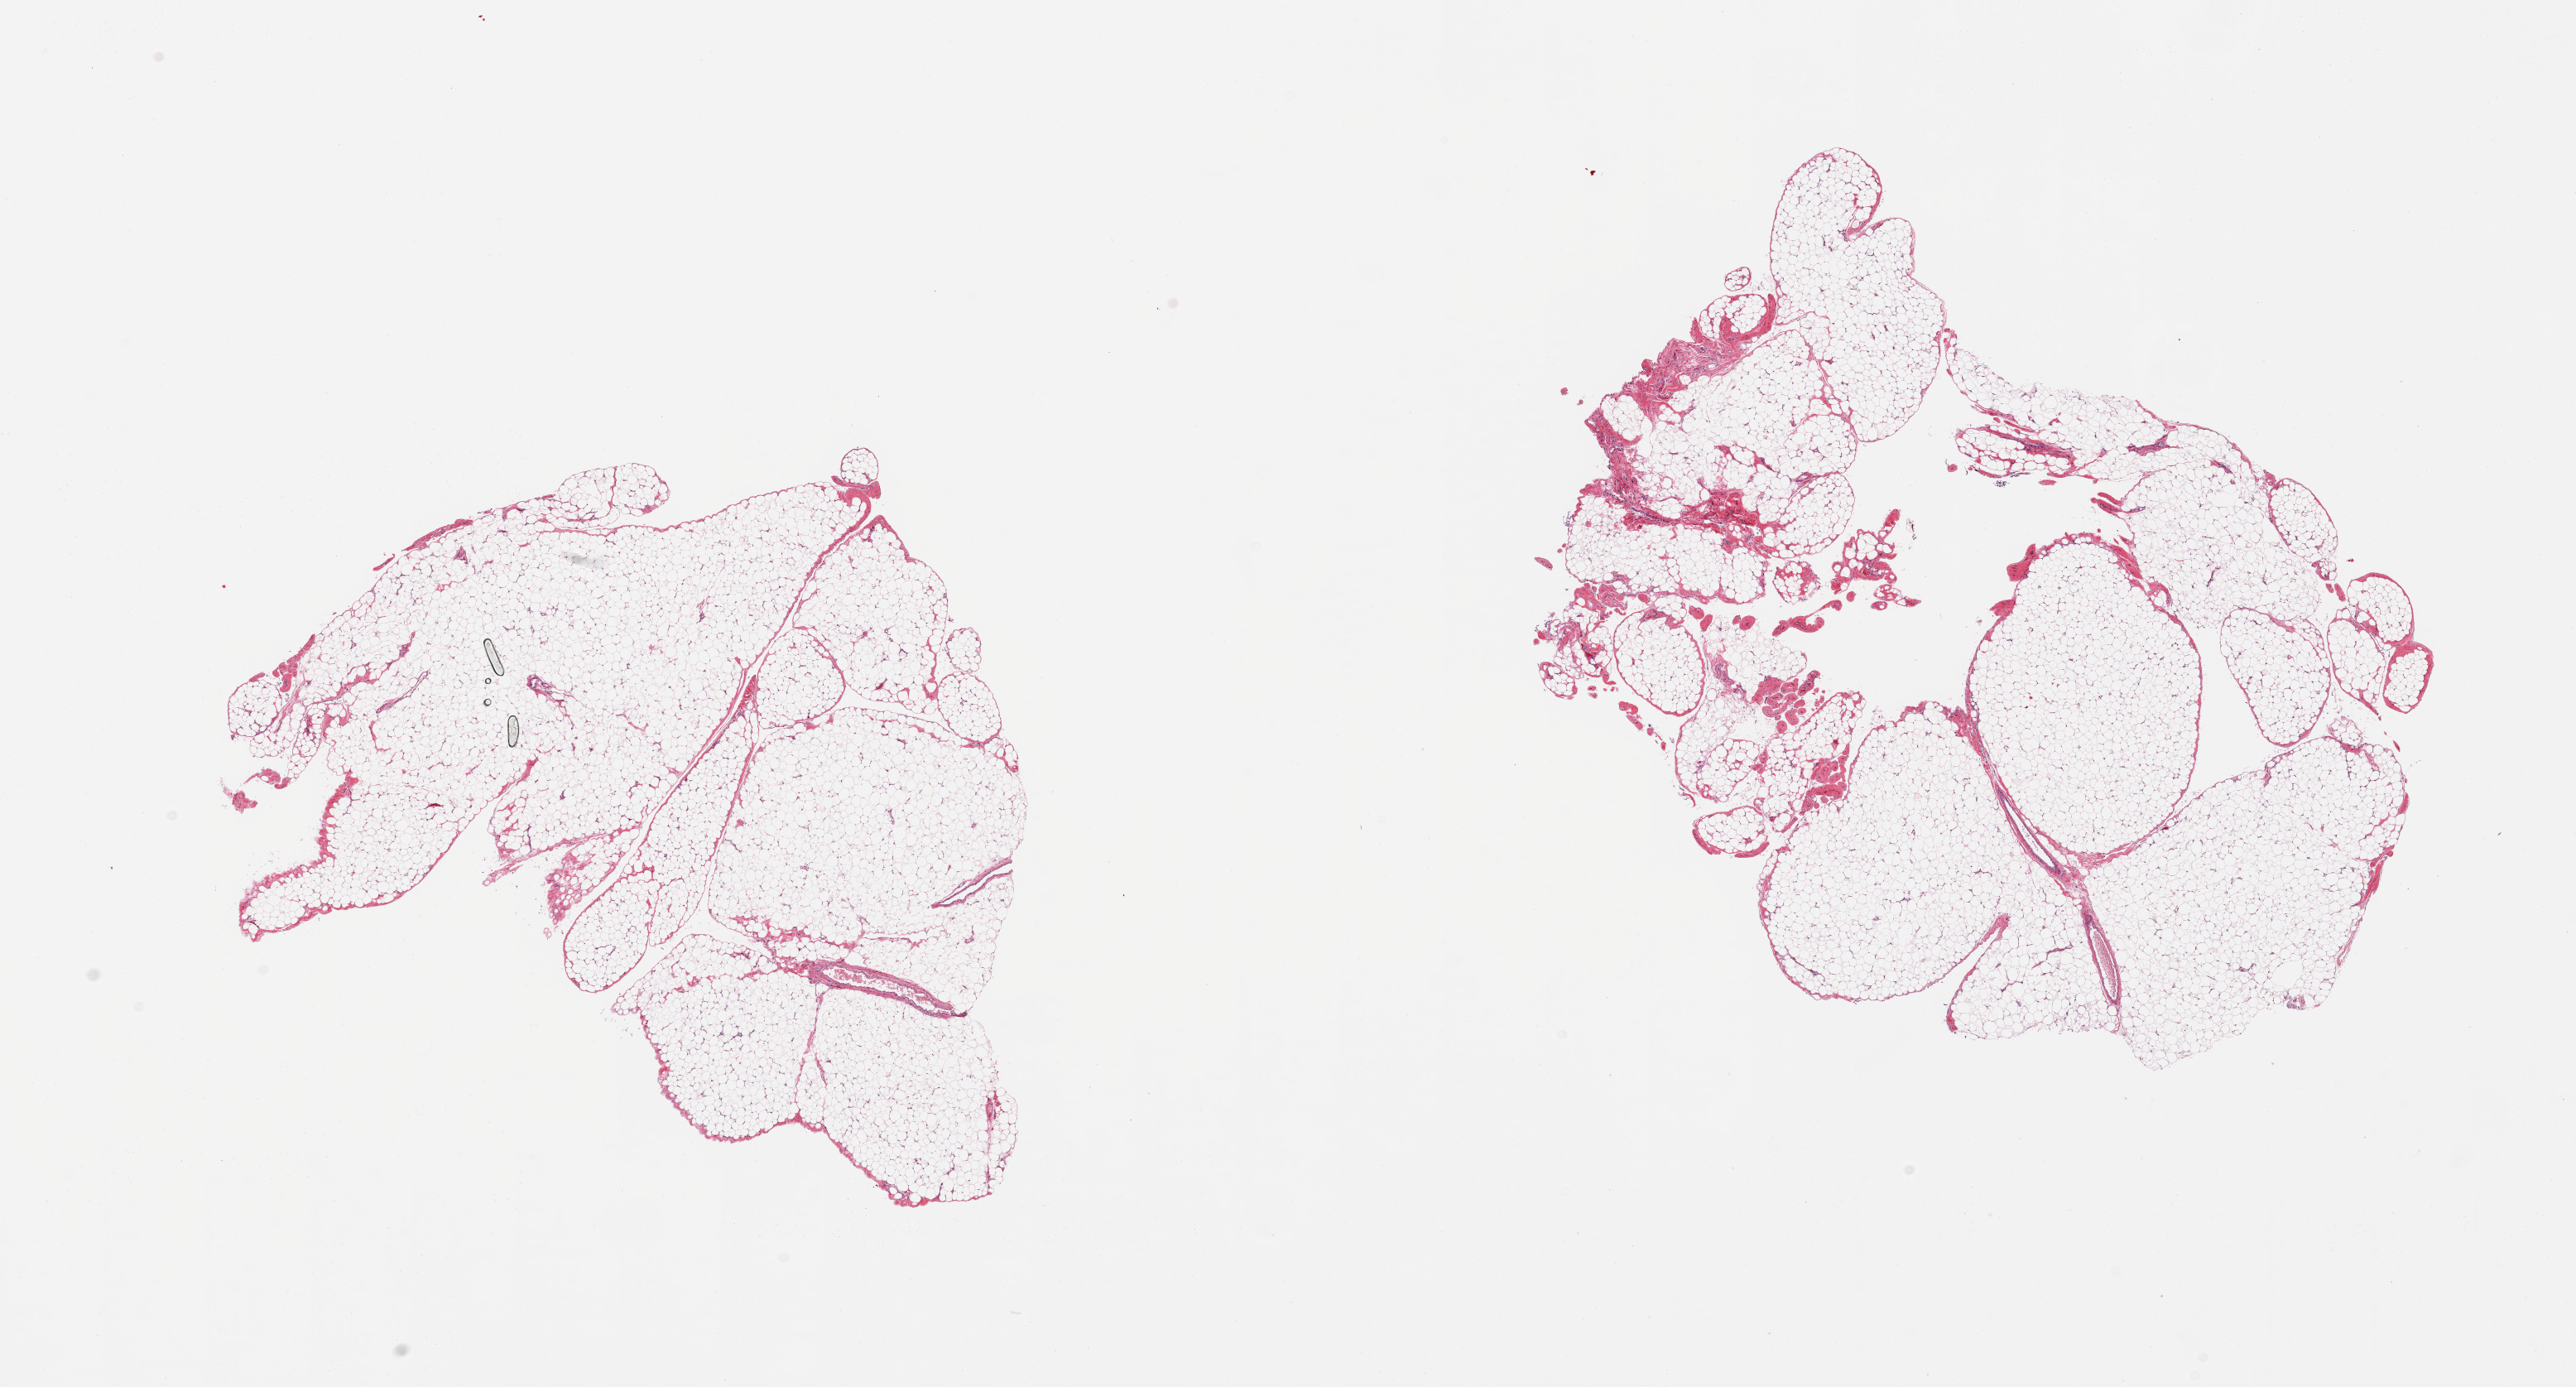
Whole-slide image, H&E stain, shown as a low-resolution overview of the whole scanned area (about 24.6 x 13.2 mm, acquisition: 20x scan); PAXgene-fixed, paraffin-embedded tissue; section of omentum (target tissue); tissue donor sample.
* reviewer comment on this tissue sample: 2 pieces; no peritonitis